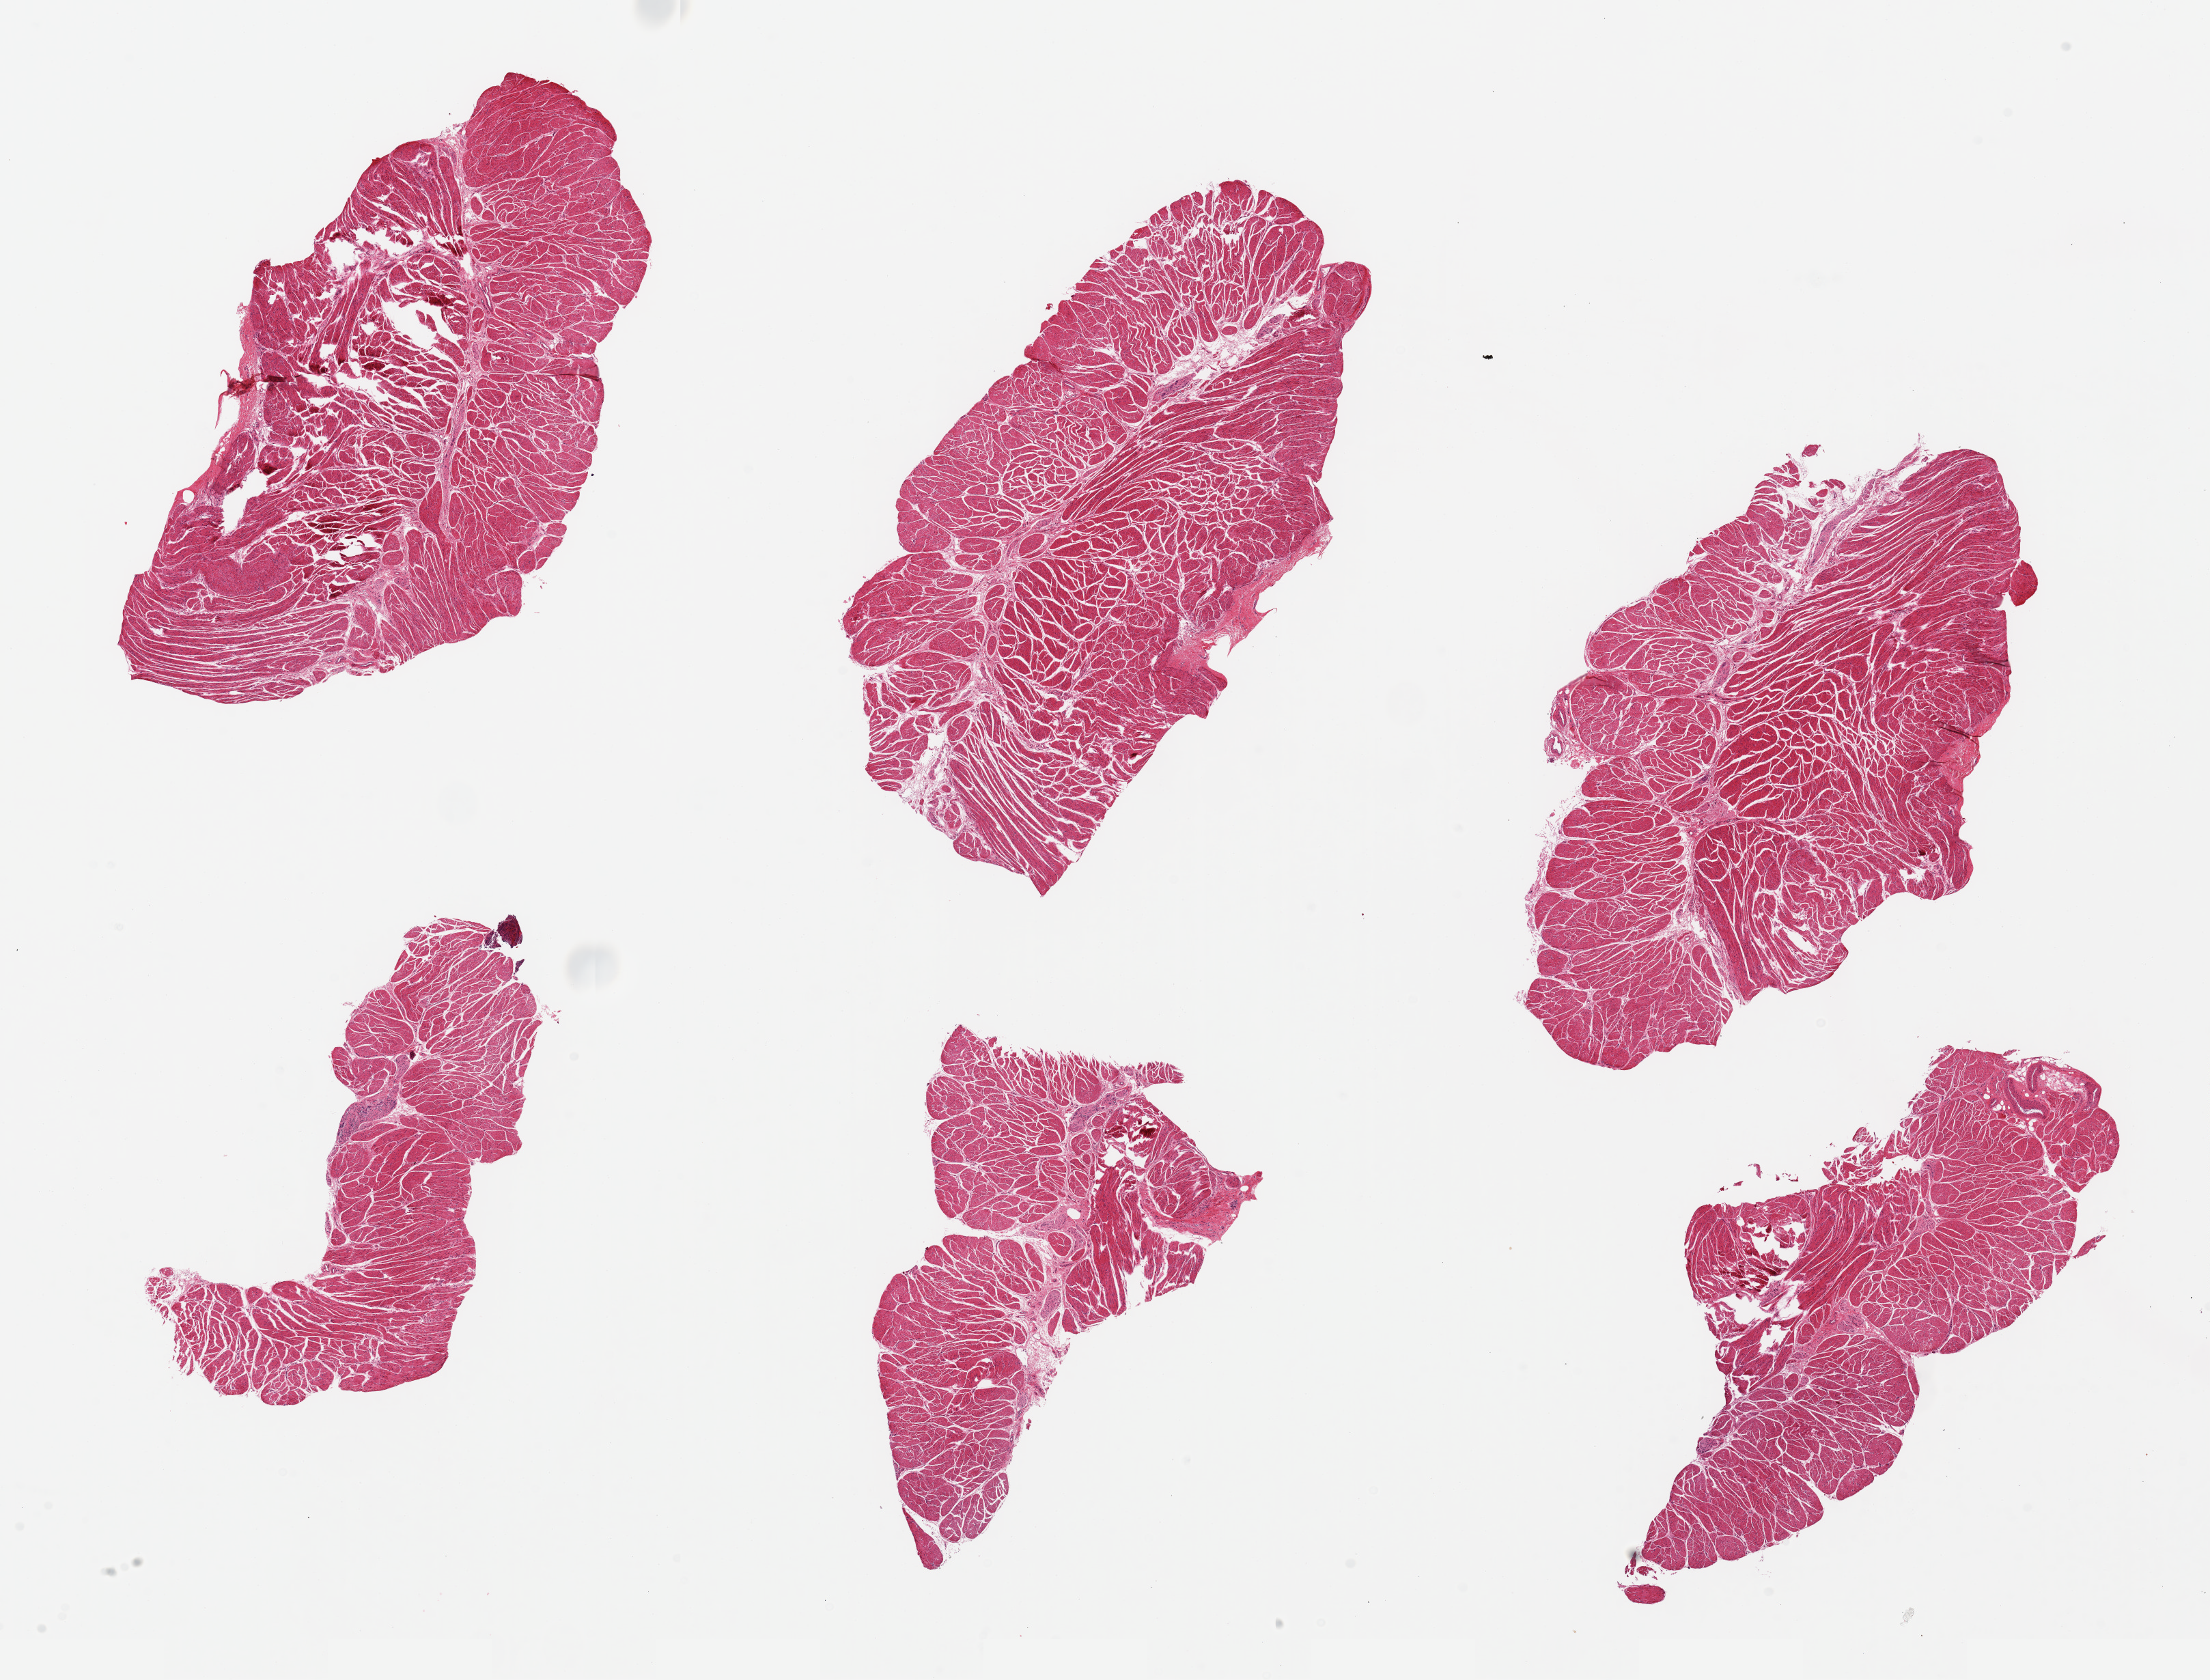
H&E whole-slide image, brightfield — shown as a low-resolution overview of the whole scanned area (about 25.6 x 19.5 mm), PAXgene-fixed paraffin-embedded (PFPE) section, target tissue: gastroesophageal junction, tissue donor sample. Donor sex: male.
* reviewer comment on this tissue sample: 6 pieces, up to 8x5mm; well sampled muscle without extraneous tissue